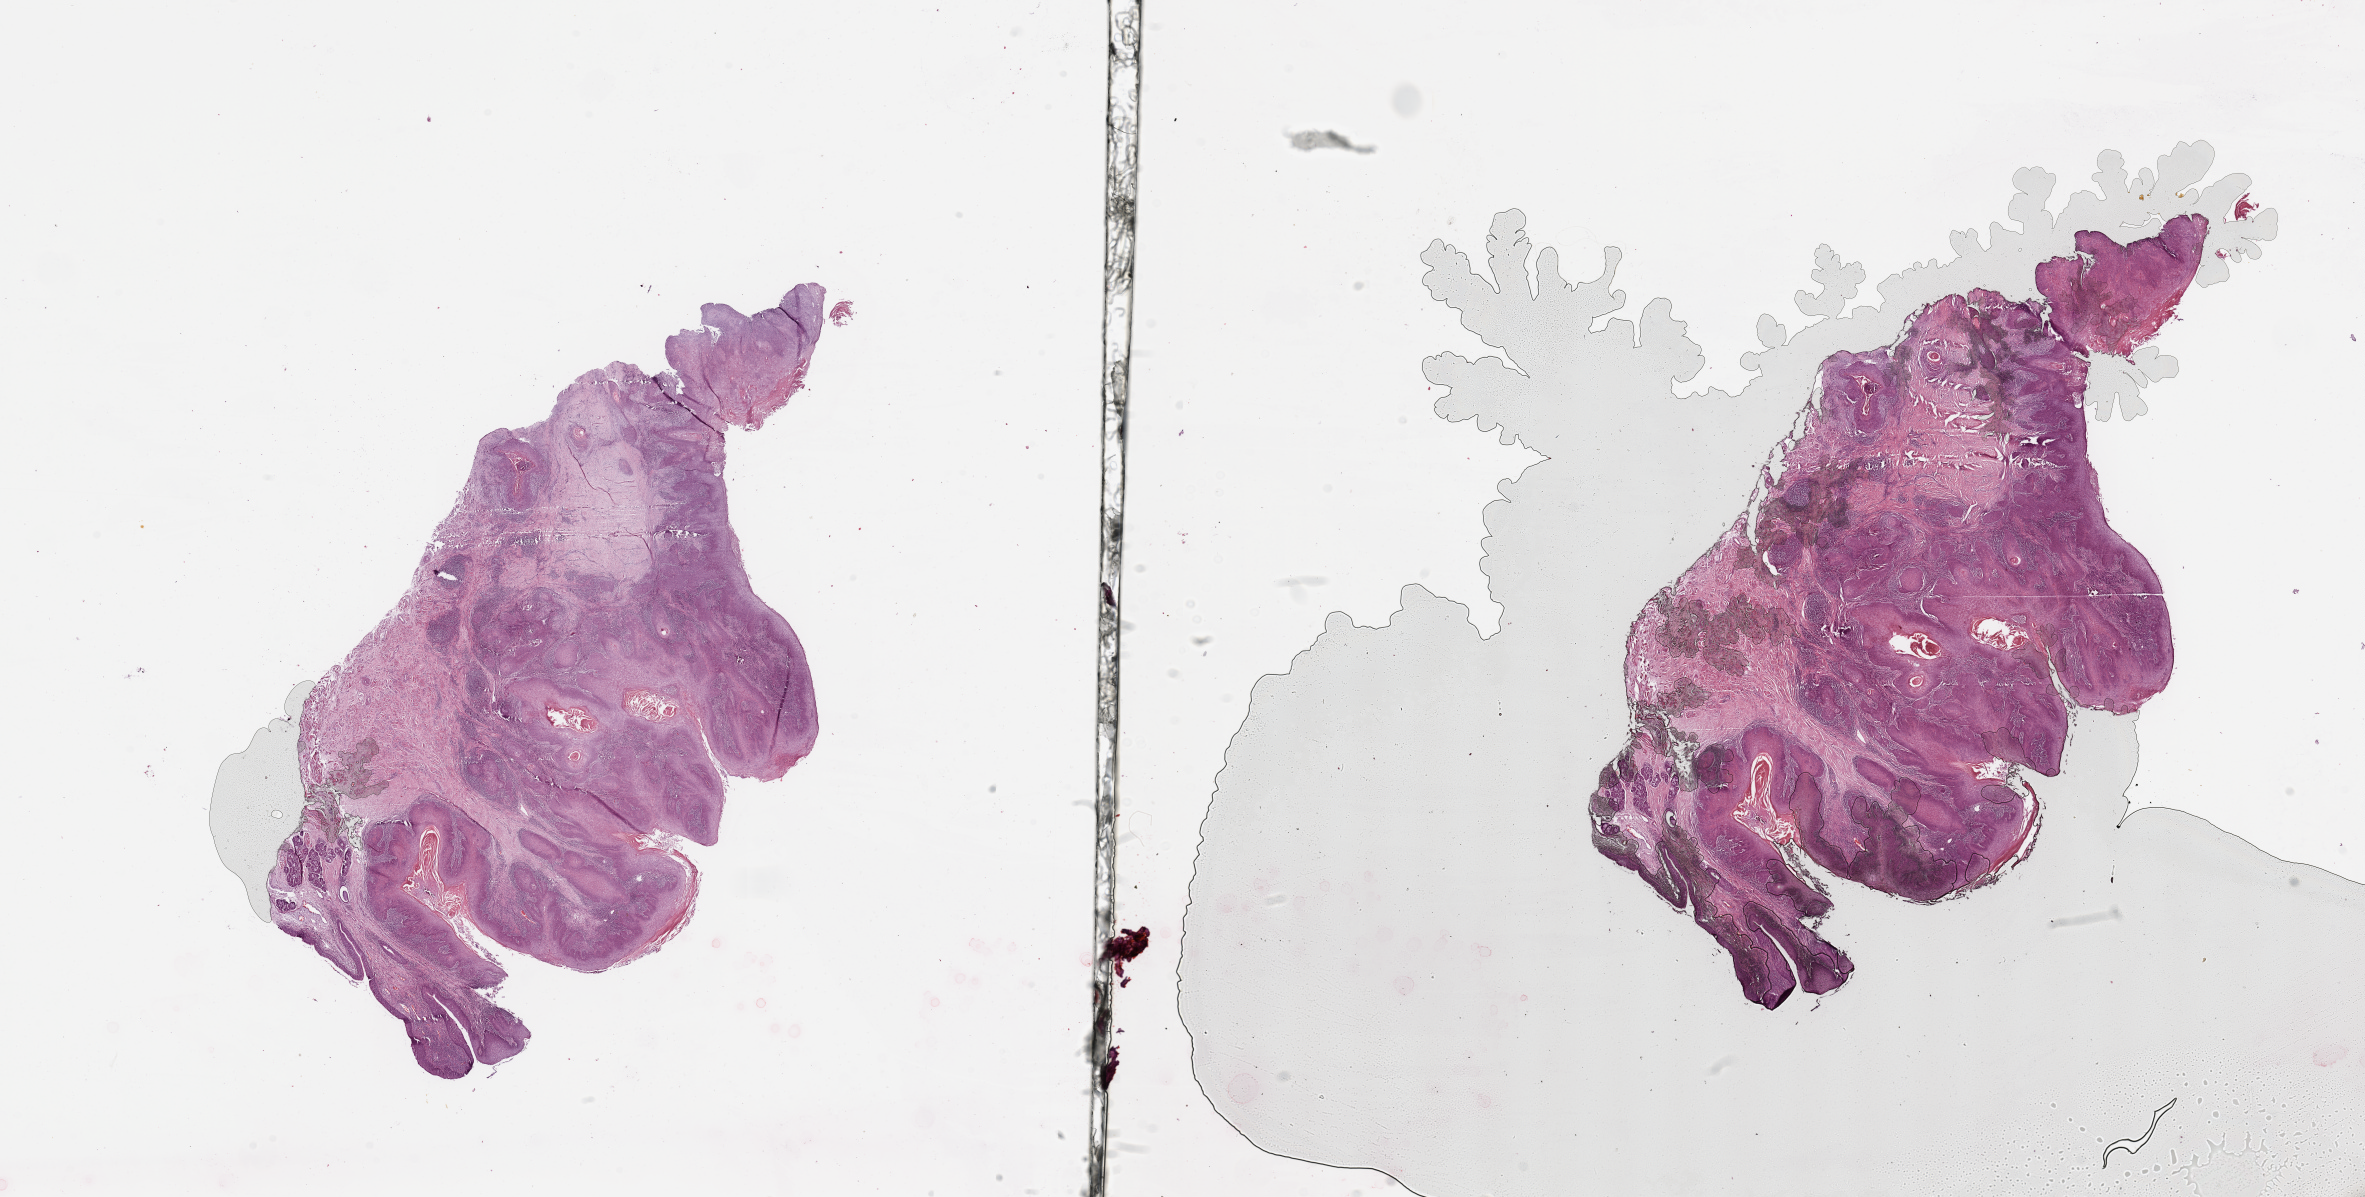
Digitized H&E-stained tissue section (whole slide), whole scanned area (about 37.4 x 18.9 mm, slide scanned at 20x) shown as a low-resolution overview. Head and neck, tissue type not recorded. 61-year-old male patient.
Patient diagnosis: Squamous cell carcinoma, NOS (larynx, NOS).